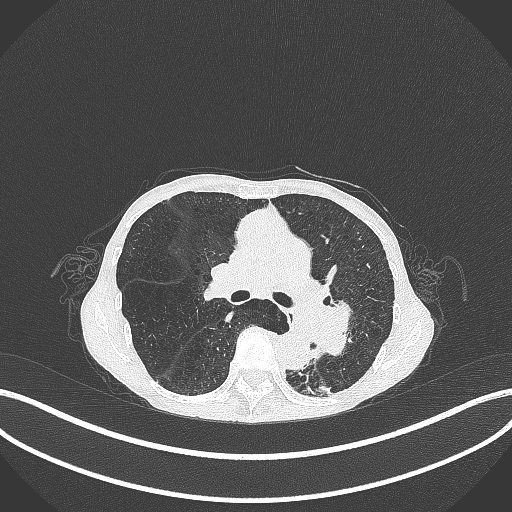
Chest CT, one axial slice; position 167 of 347 along the scan axis; 120 kVp; lung window (W 1500 / L -600 HU); 1 mm slice thickness; 512 × 512 image matrix, field of view 400 × 400 mm. Patient: female, 70 years. Case-level facts recorded for this patient, not image findings: clinical TNM (as recorded): T3 N0 M0.
Outlined on this slice (rectangle marked by the reading radiologist):
- lung tumour (recorded histology: small cell carcinoma): bounding box [x1, y1, x2, y2] px = [298, 292, 360, 362]